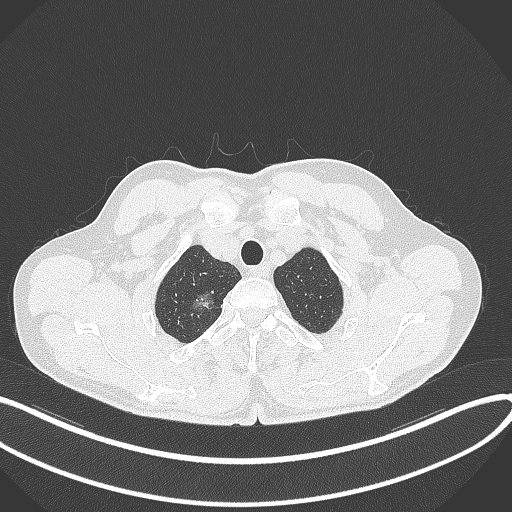
Chest CT, one axial slice; position 344 of 407 along the scan axis; reconstruction kernel B70f; lung window (W 1500 / L -600 HU); 1 mm slice thickness; 512 × 512 image matrix, field of view 400 × 400 mm. Male patient, age 58 years. Case-level facts recorded for this patient, not image findings: clinical TNM (as recorded): T1c N0 M0; histopathological grade: G1-2.
Outlined on this slice (rectangle marked by the reading radiologist):
- lung tumour (recorded histology: adenocarcinoma): bounding box (x1, y1, x2, y2) in pixels: (187, 289, 218, 318)